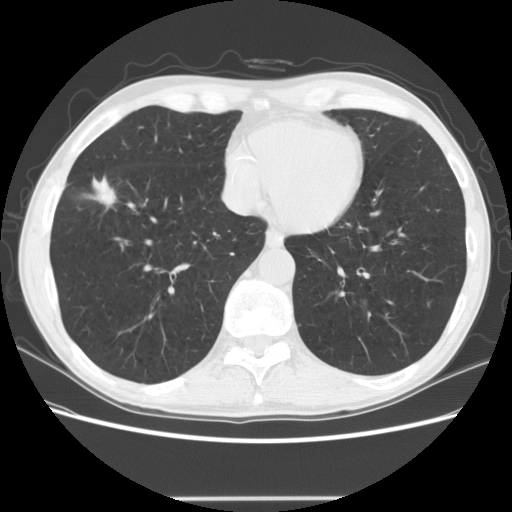
Low-dose screening chest CT, axial slice. Baseline annual screen. Lung window (W 1500 / L -600 HU). 2.5 mm slice thickness. Standard (soft-tissue) reconstruction kernel (STANDARD). Slice 96 of 145 in the series. Male participant, aged 69 years at enrolment. Current smoker at enrolment.
Expert reader's lesion annotation, box from (x=74, y=163) to (x=127, y=212) px. The exam's reader record, not a measurement of the box and not confirmed to be the same lesion: non-calcified nodule or mass ≥4 mm, right middle lobe, 20 × 14 mm, spiculated (stellate) margins, mixed attenuation. Lung cancer was diagnosed 86 days after this screen: squamous cell carcinoma, NOS, right middle lobe, poorly differentiated (G3), stage IA (AJCC 6th edition), 15 mm at pathology.